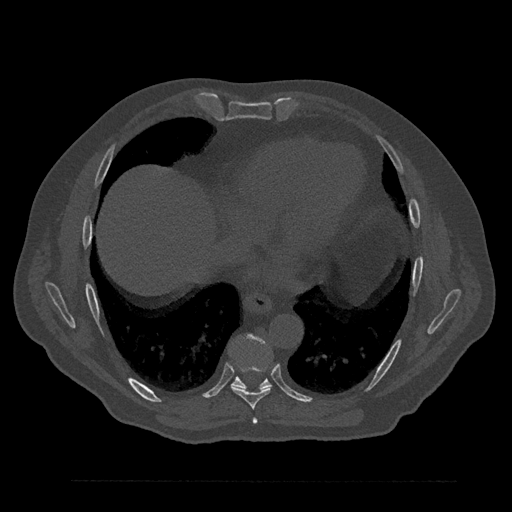
CT including the spine, one axial slice. Slice 437 of 797 in the series (ordered by position). Reconstruction kernel Br40s/3. 120 kVp. Bone window (W 1800 / L 400 HU). 0.5 mm slice thickness. 512 × 512 image matrix. Male patient, age 61 years. From the clinical record (not read from this slice): primary cancer: prostate.
Outlined on this slice (semi-automatic segmentation, software-assisted and operator-edited):
- T7 vertebra: bounding box <252,418,257,424> (left, top, right, bottom; pixels)
- T8 vertebra: <231,367,272,409>
- T9 vertebra: <232,334,272,389>